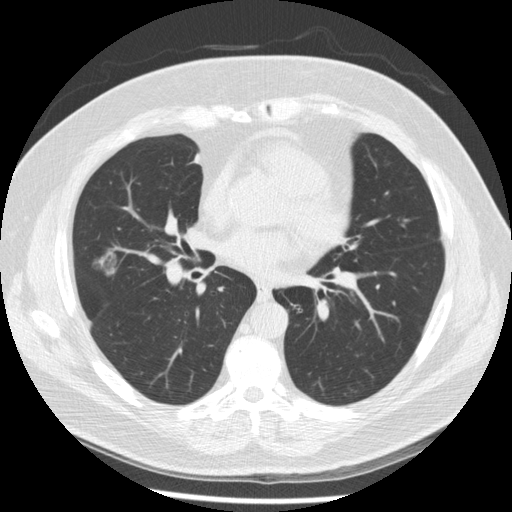
Low-dose screening chest CT, axial slice. Second annual screen. Lung window (W 1500 / L -600 HU). 2.5 mm slice thickness. Slice 119 of 230 in the series. 512 × 512 image matrix, field of view 360 × 360 mm. Male participant, aged 67 years at enrolment. Former smoker at enrolment.
- Expert-annotated lung lesion, bounding box [x1, y1, x2, y2] px = [79, 244, 124, 287].
- The exam's reader record, not a measurement of the box and not confirmed to be the same lesion: non-calcified nodule or mass ≥4 mm, right middle lobe, 19 × 16 mm, smooth margins, soft tissue attenuation, pre-existing on the prior screen: yes; interval growth: yes.
- Lung cancer was diagnosed 47 days after this screen: adenocarcinoma, NOS, right middle lobe, moderately differentiated (G2), stage IA (AJCC 6th edition), 14 mm at pathology.